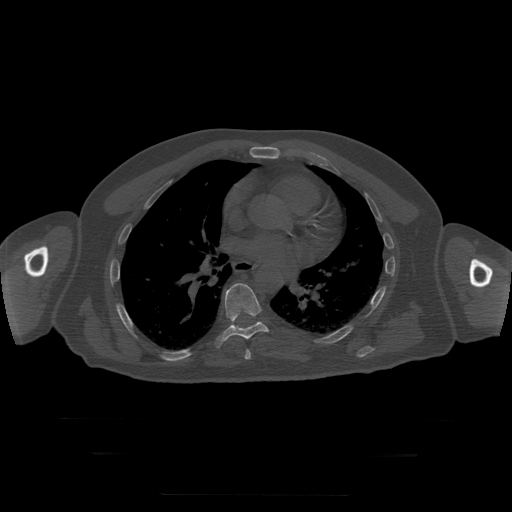
CT including the spine, one axial slice; slice 167 of 397 in the series (ordered by position); reconstruction kernel STANDARD; 120 kVp; bone window (W 1800 / L 400 HU); 1.25 mm slice thickness; 512 × 512 image matrix, field of view 510 × 510 mm. Patient age 73 years. From the clinical record (not read from this slice): primary cancer: prostate.
Annotated regions visible in this slice (semi-automatic segmentation, software-assisted and operator-edited):
- T7 vertebra: bounding box [x1, y1, x2, y2] px = [245, 350, 251, 360]
- T8 vertebra: [214, 283, 278, 349]